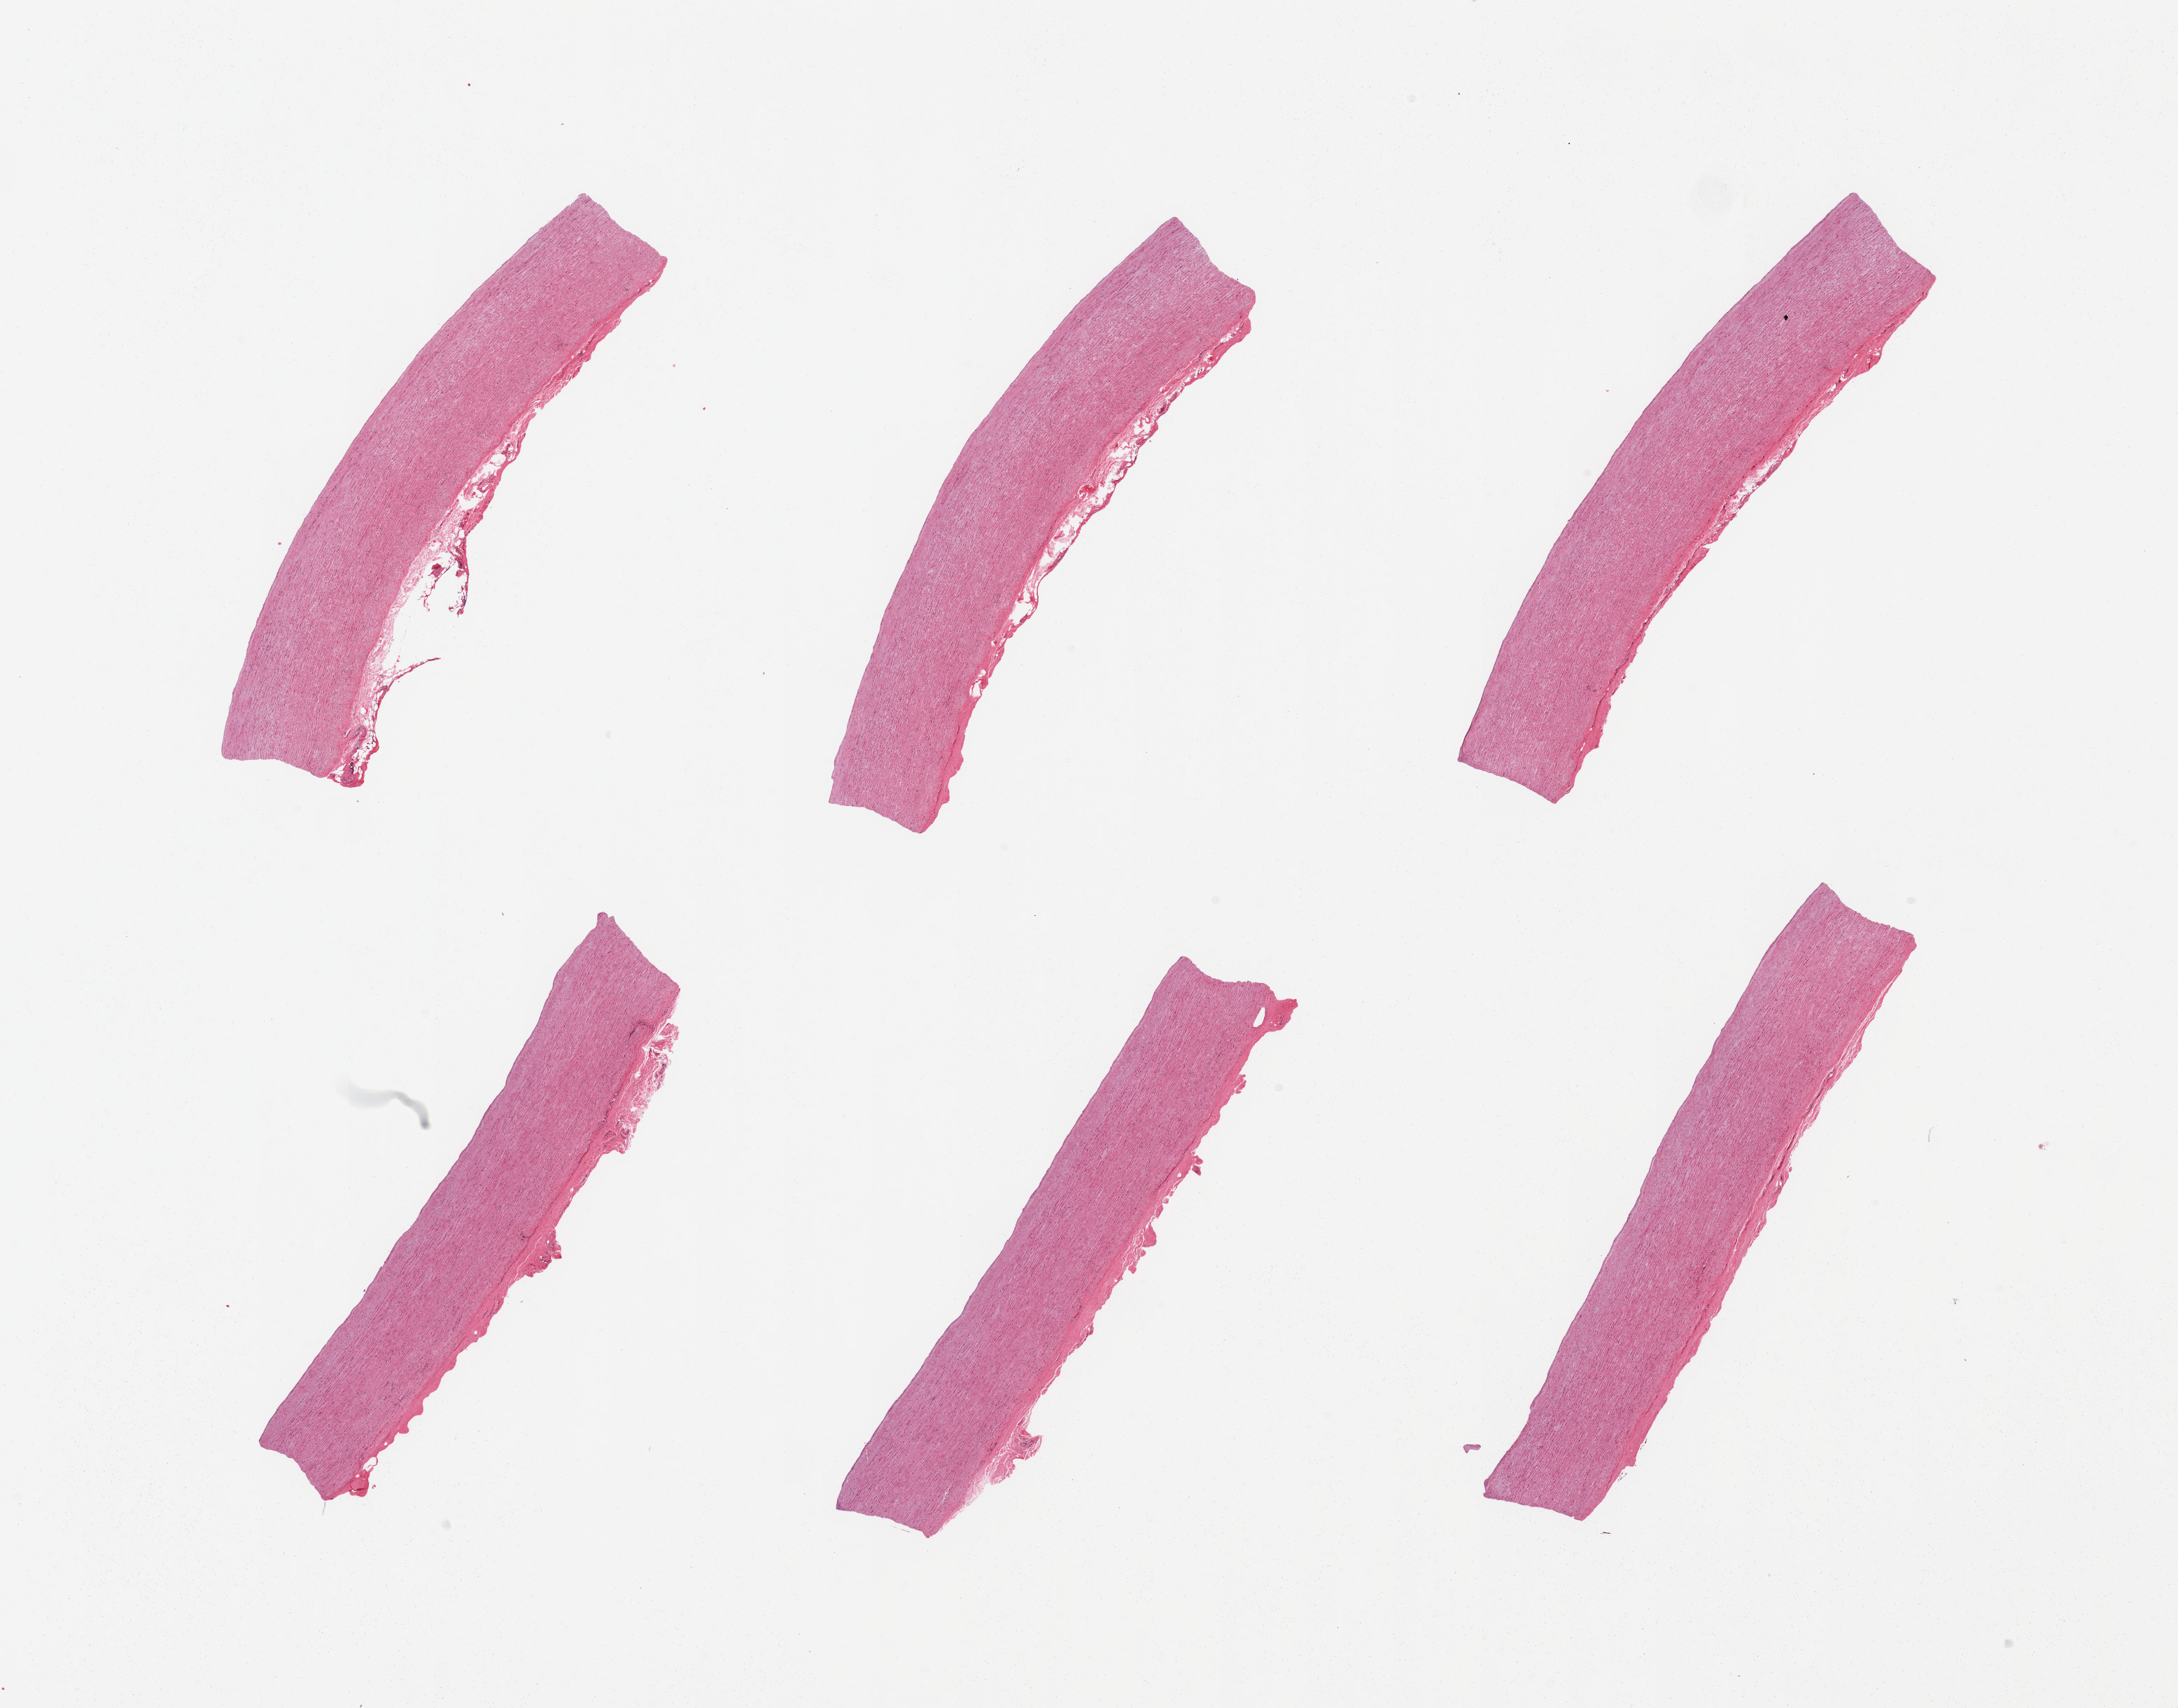
Hematoxylin and eosin (H&E) whole-slide image, shown as a low-resolution overview of the whole scanned area (about 24.6 x 19.3 mm, acquisition: 20x scan). PAXgene-fixed paraffin-embedded (PFPE) section. Section of aorta (target tissue). Tissue donor sample.
* pathologist's review note for this sample: 6 pieces, minmal atherosis